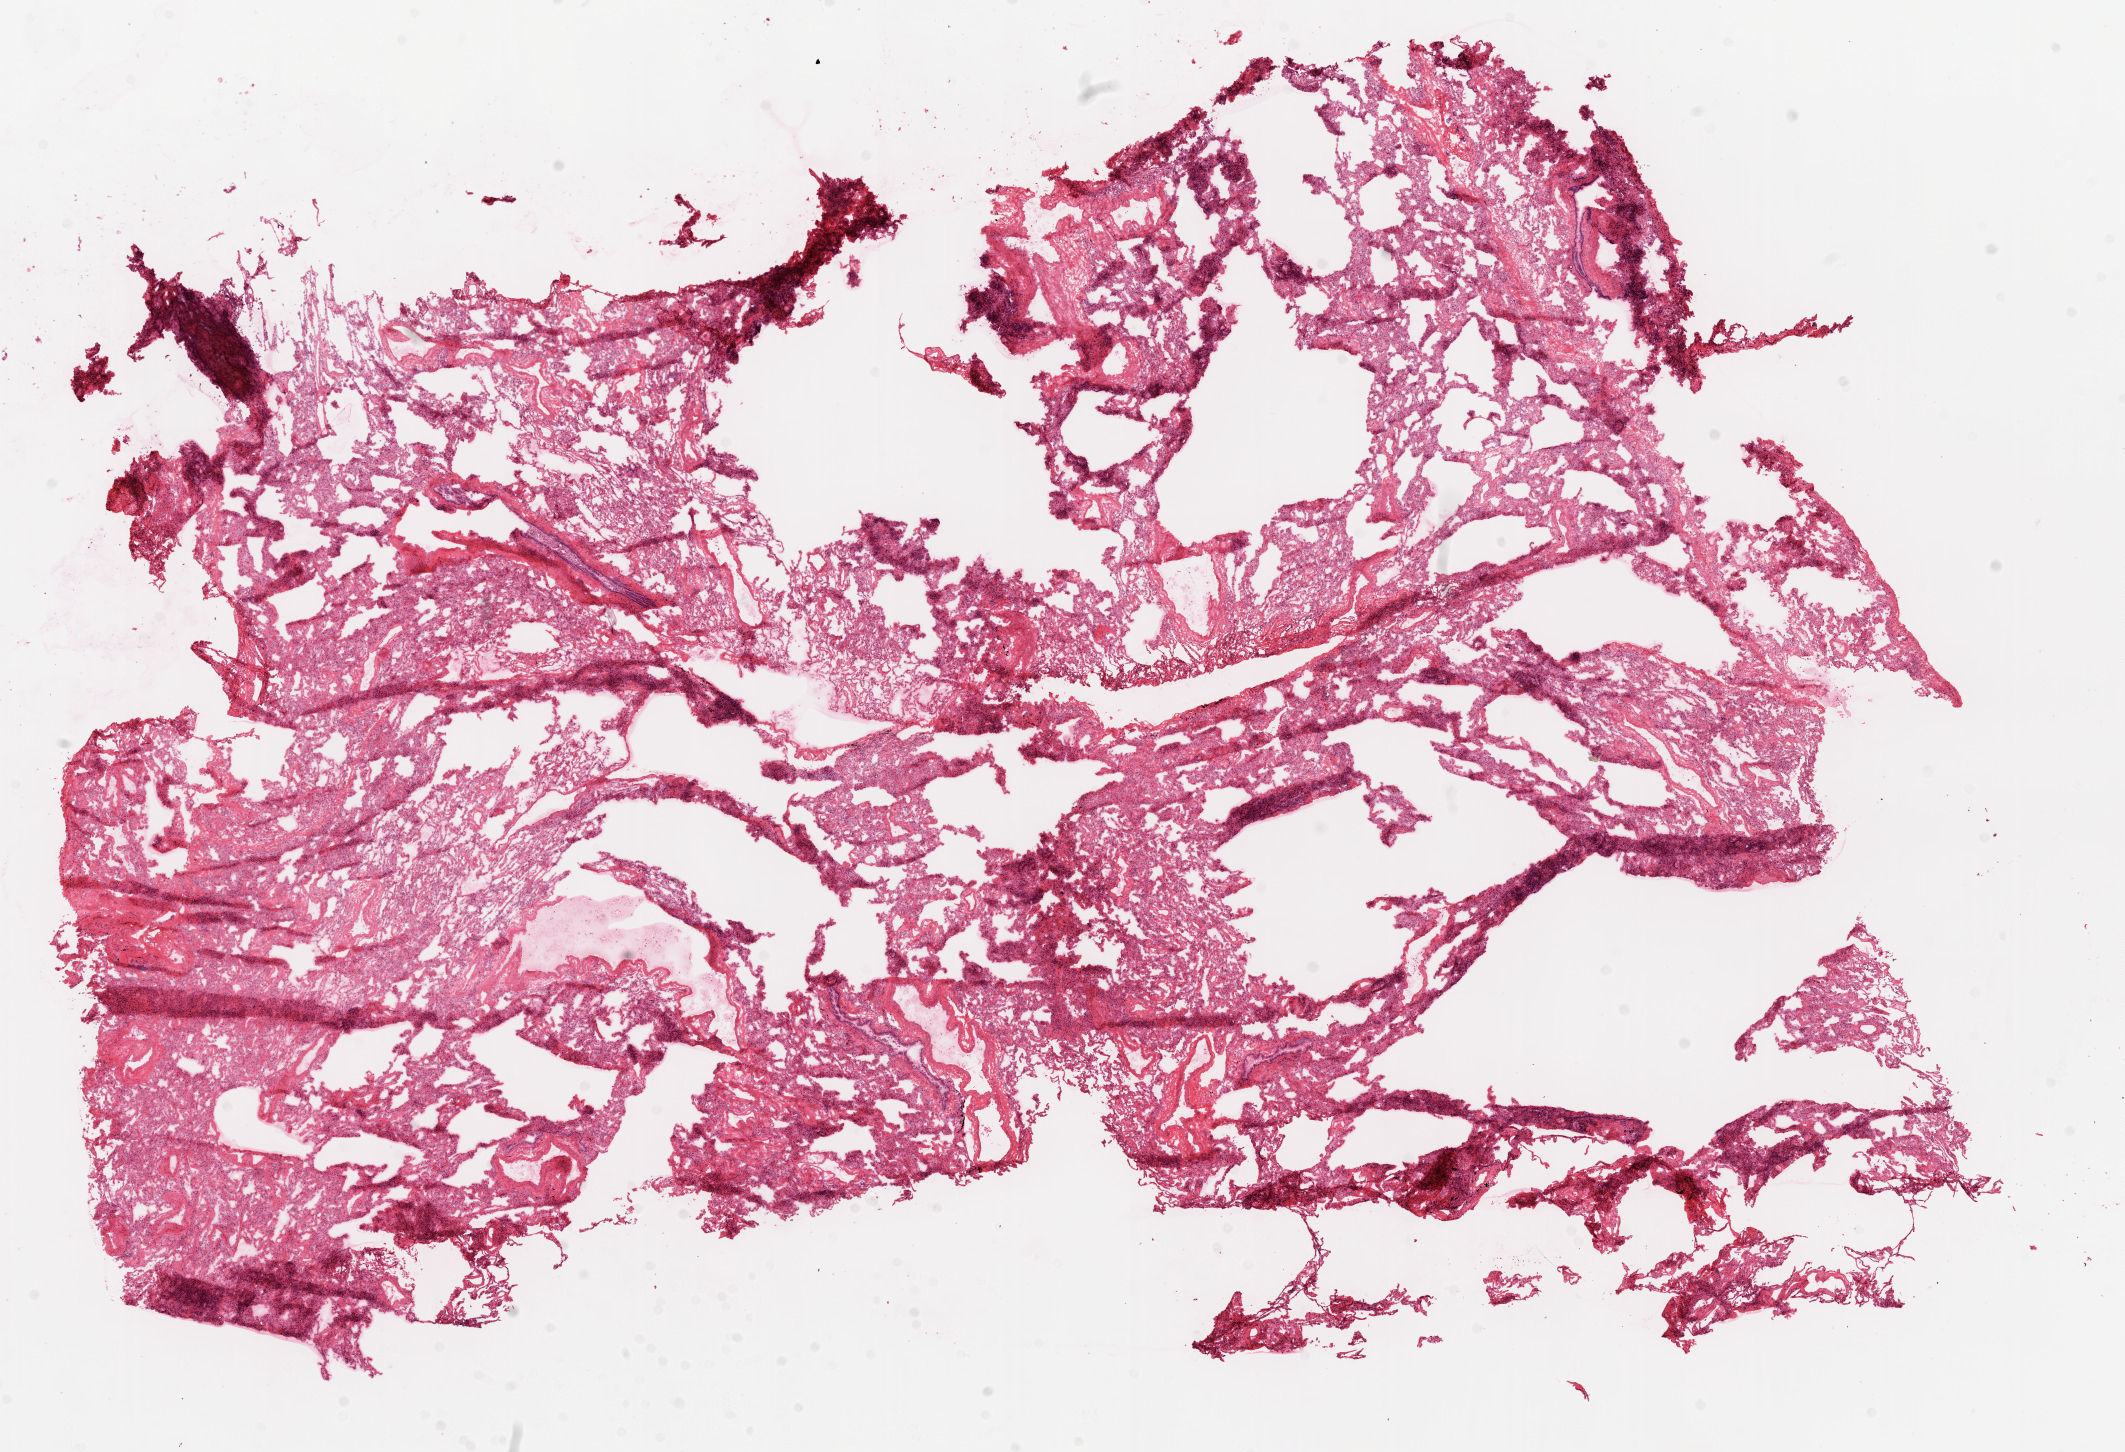
Digitized H&E tissue section (whole slide), a low-resolution overview of the entire scanned area, about 17.1 x 11.7 mm (acquisition: 20x scan), frozen section from the top of the tissue portion, solid tissue normal (non-tumour tissue) sample from the lung. Patient: female, age at initial diagnosis 70 years.
This section: solid tissue normal (non-tumour) sample from the same patient. Patient diagnosis: Squamous cell carcinoma, NOS.